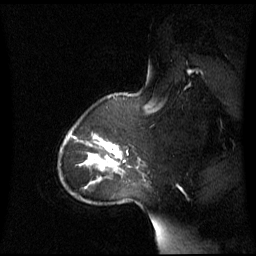
Breast MRI (dynamic contrast-enhanced), one sagittal slice; slice 49 of 60 in the series (ordered by position); dynamic contrast-enhanced series, image 2 of 3 at this slice position (ordered by acquisition); 1.5 T; TE 4.2 ms, TR 8.4 ms; 2.8 mm slice thickness; 256 × 256 image matrix, field of view 270 × 270 mm. Female patient, age 43 years. Case-level facts recorded for this patient, not image findings: setting: breast cancer imaged before/during neoadjuvant chemotherapy; receptor status: triple-negative.
Structures marked on this image (semi-automatic segmentation, software-assisted and operator-edited):
- analysis volume of interest (the breast-tissue region the enhancement analysis was run in; not a lesion): bounding box (x1, y1, x2, y2) in pixels: (62, 124, 137, 180)
- tumour enhancement mask (voxels above the 70 % enhancement threshold inside the analysis volume of interest): (91, 135, 122, 170)